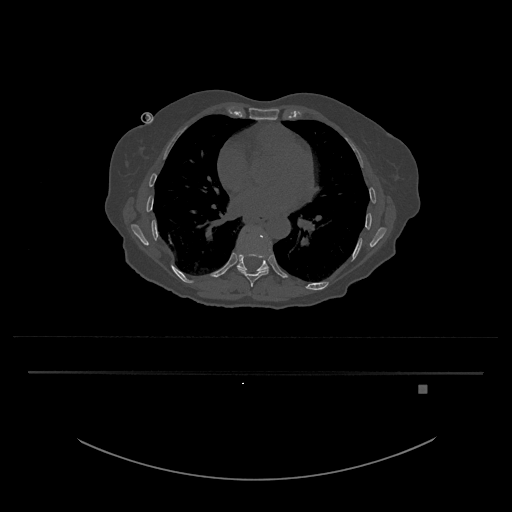
CT including the spine, one axial slice. Position 742 of 797 along the scan axis. 120 kVp. Bone window (W 1800 / L 400 HU). 0.5 mm slice thickness. 512 × 512 image matrix, field of view 500 × 500 mm. Patient: female, 57 years. From the clinical record (not read from this slice): primary cancer: cervical.
Structures marked on this image (semi-automatically segmented with operator editing):
- T10 vertebra: bounding box <237,227,269,272> (left, top, right, bottom; pixels)
- T9 vertebra: <238,245,269,287>